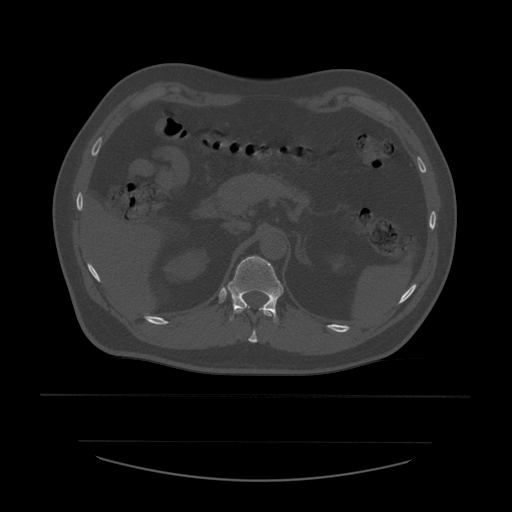
CT including the spine, one axial slice. Position 259 of 532 along the scan axis. Reconstruction kernel STANDARD. Bone window (W 1800 / L 400 HU). 1.25 mm slice thickness. 512 × 512 image matrix, field of view 441 × 441 mm. Patient age 44 years. From the clinical record (not read from this slice): primary cancer: soft tissue sarcoma.
Outlined on this slice (semi-automatically segmented with operator editing):
- T11 vertebra: bounding box <235,309,274,343> (left, top, right, bottom; pixels)
- T12 vertebra: <227,256,284,323>